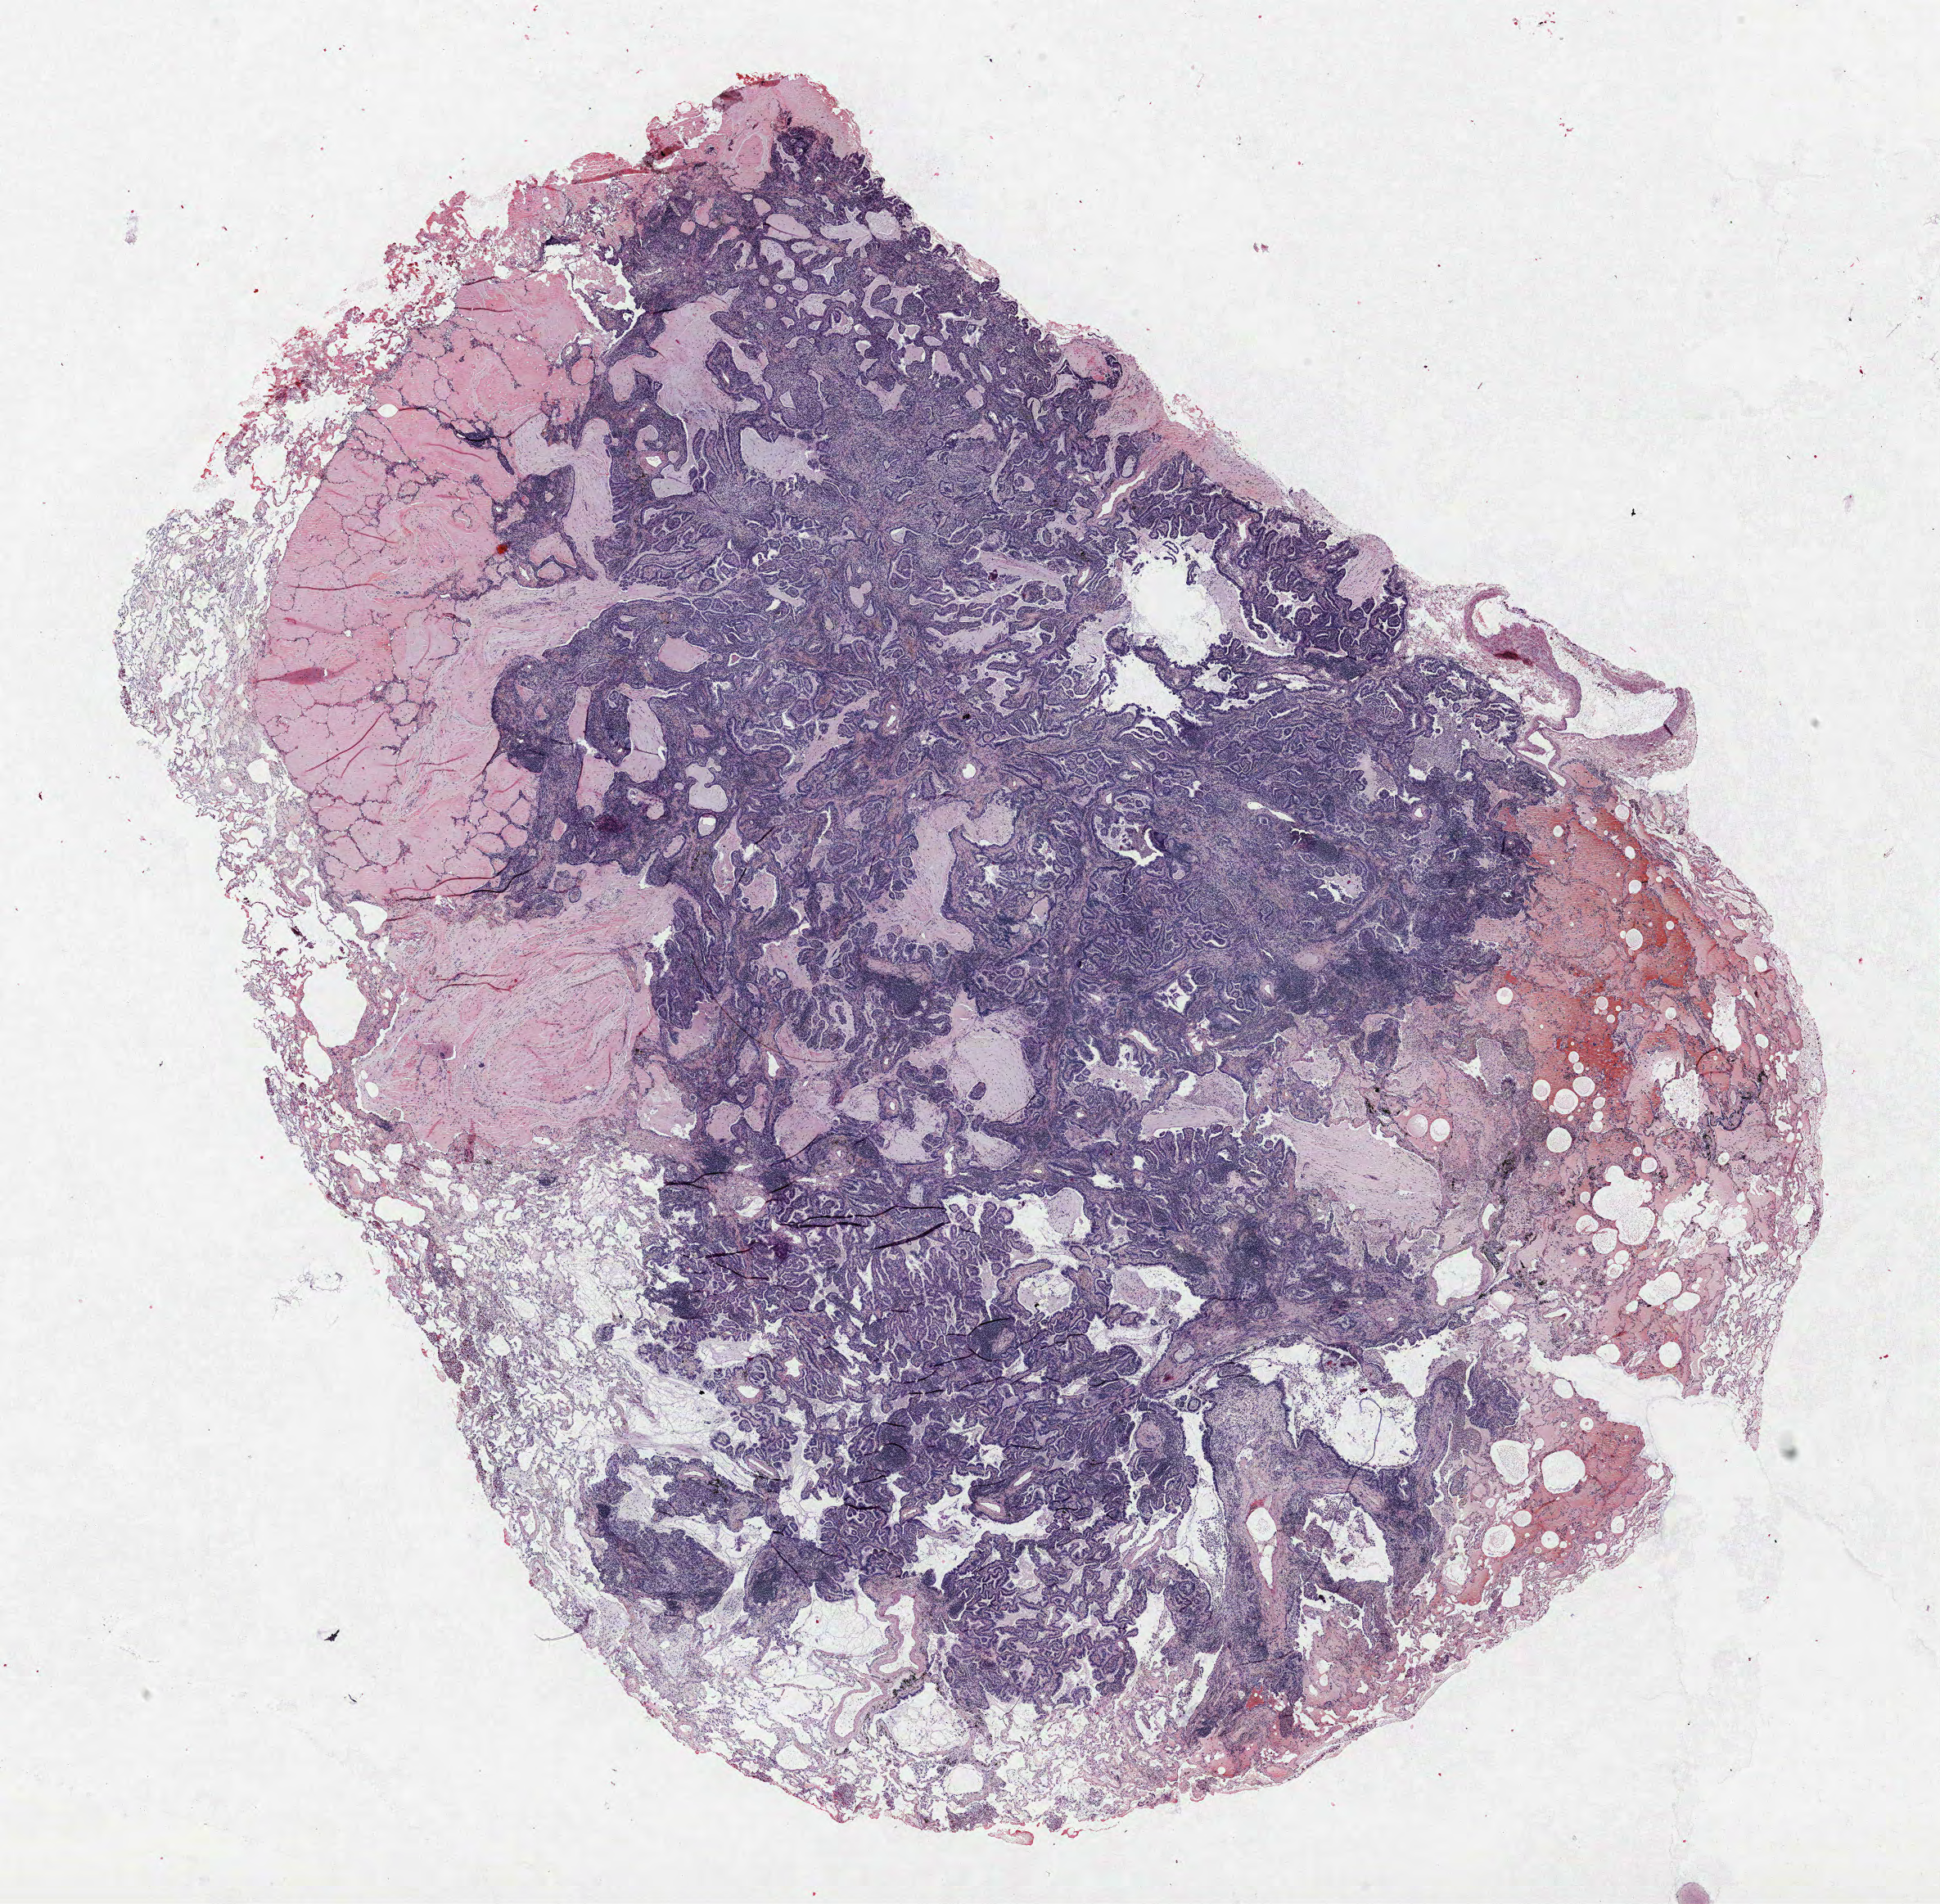
Hematoxylin and eosin (H&E) stained whole-slide image — low-resolution overview of the scanned area, about 19.0 x 18.6 mm, FFPE section, lung tissue. Male, age 72 at enrolment. Grade: moderately differentiated (G2).
- tumour size (pathology): 15 mm
- stage (AJCC 6th edition): IA
- primary tumour location (clinical record): right upper lobe
- participant's lung-cancer diagnosis: Mucin-producing adenocarcinoma (ICD-O-3 8481/3)